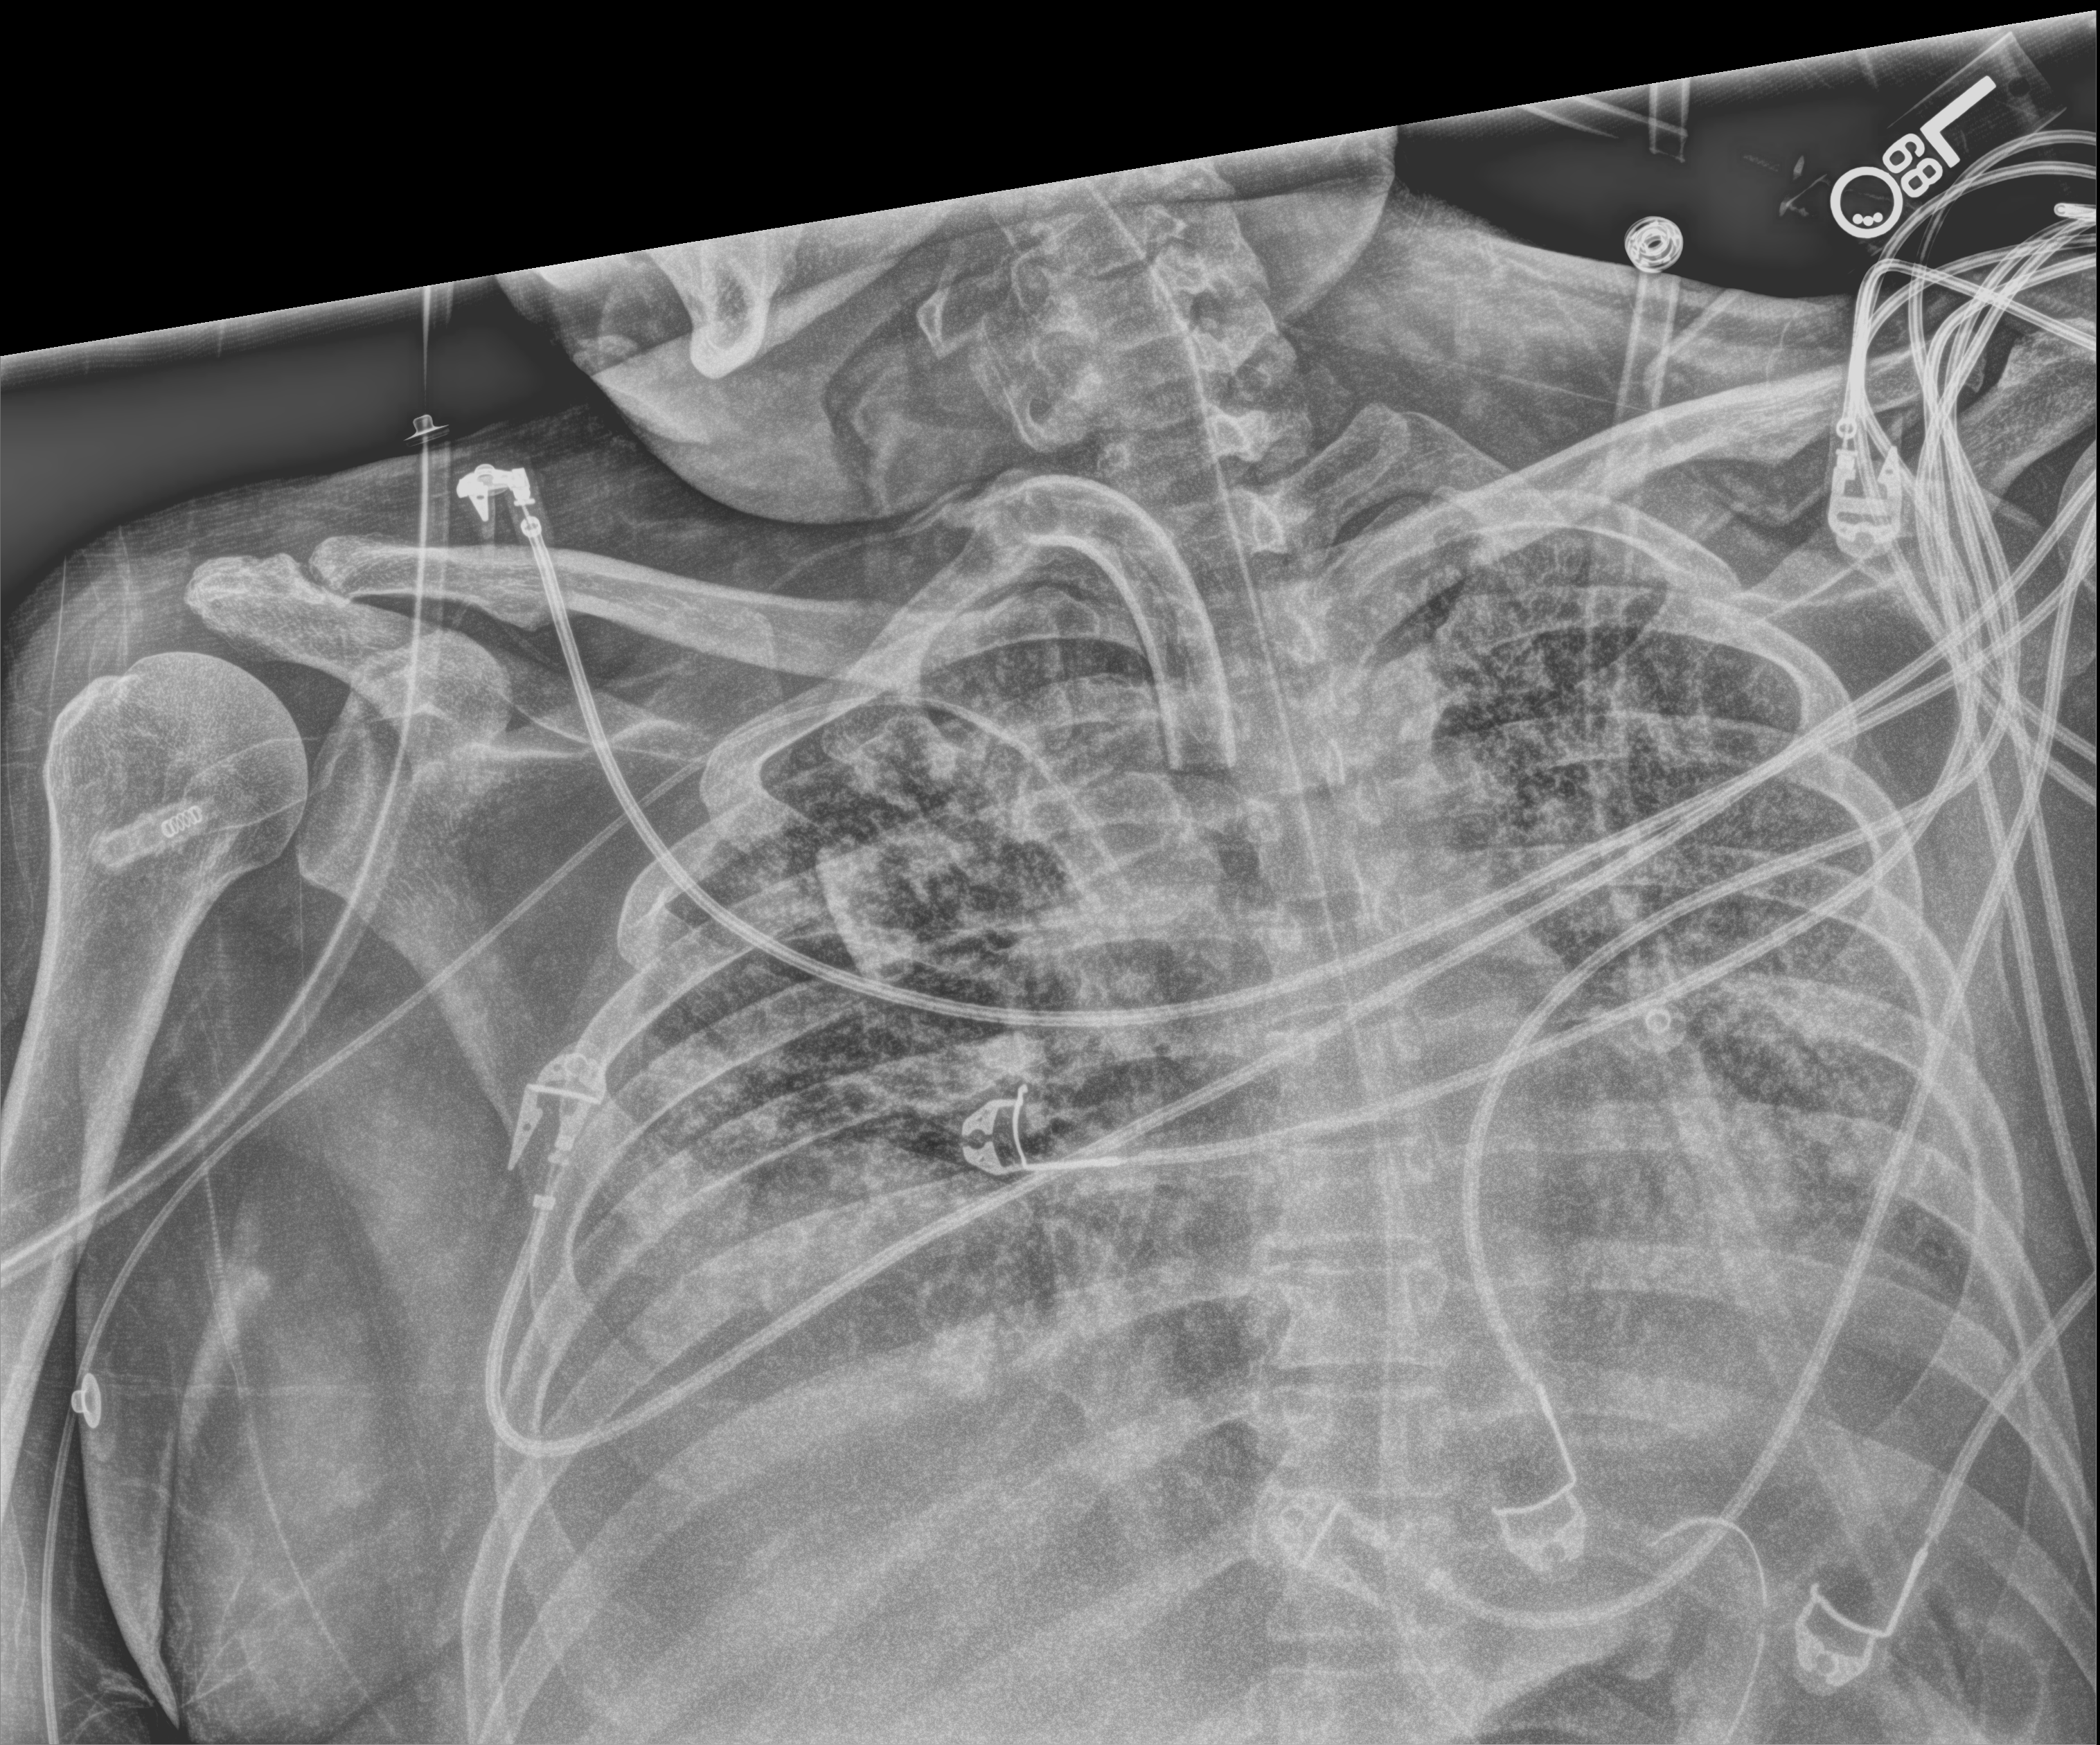
Chest X-ray (portable); anteroposterior (AP) projection. Patient hospitalised with COVID-19; male, aged 18–59 years.
Admission-level facts for this patient (not findings on this image; timing relative to this image not recorded): mechanically ventilated during this hospital stay: yes; diabetes (admission record): no; admitted to intensive care during this hospital stay: yes.